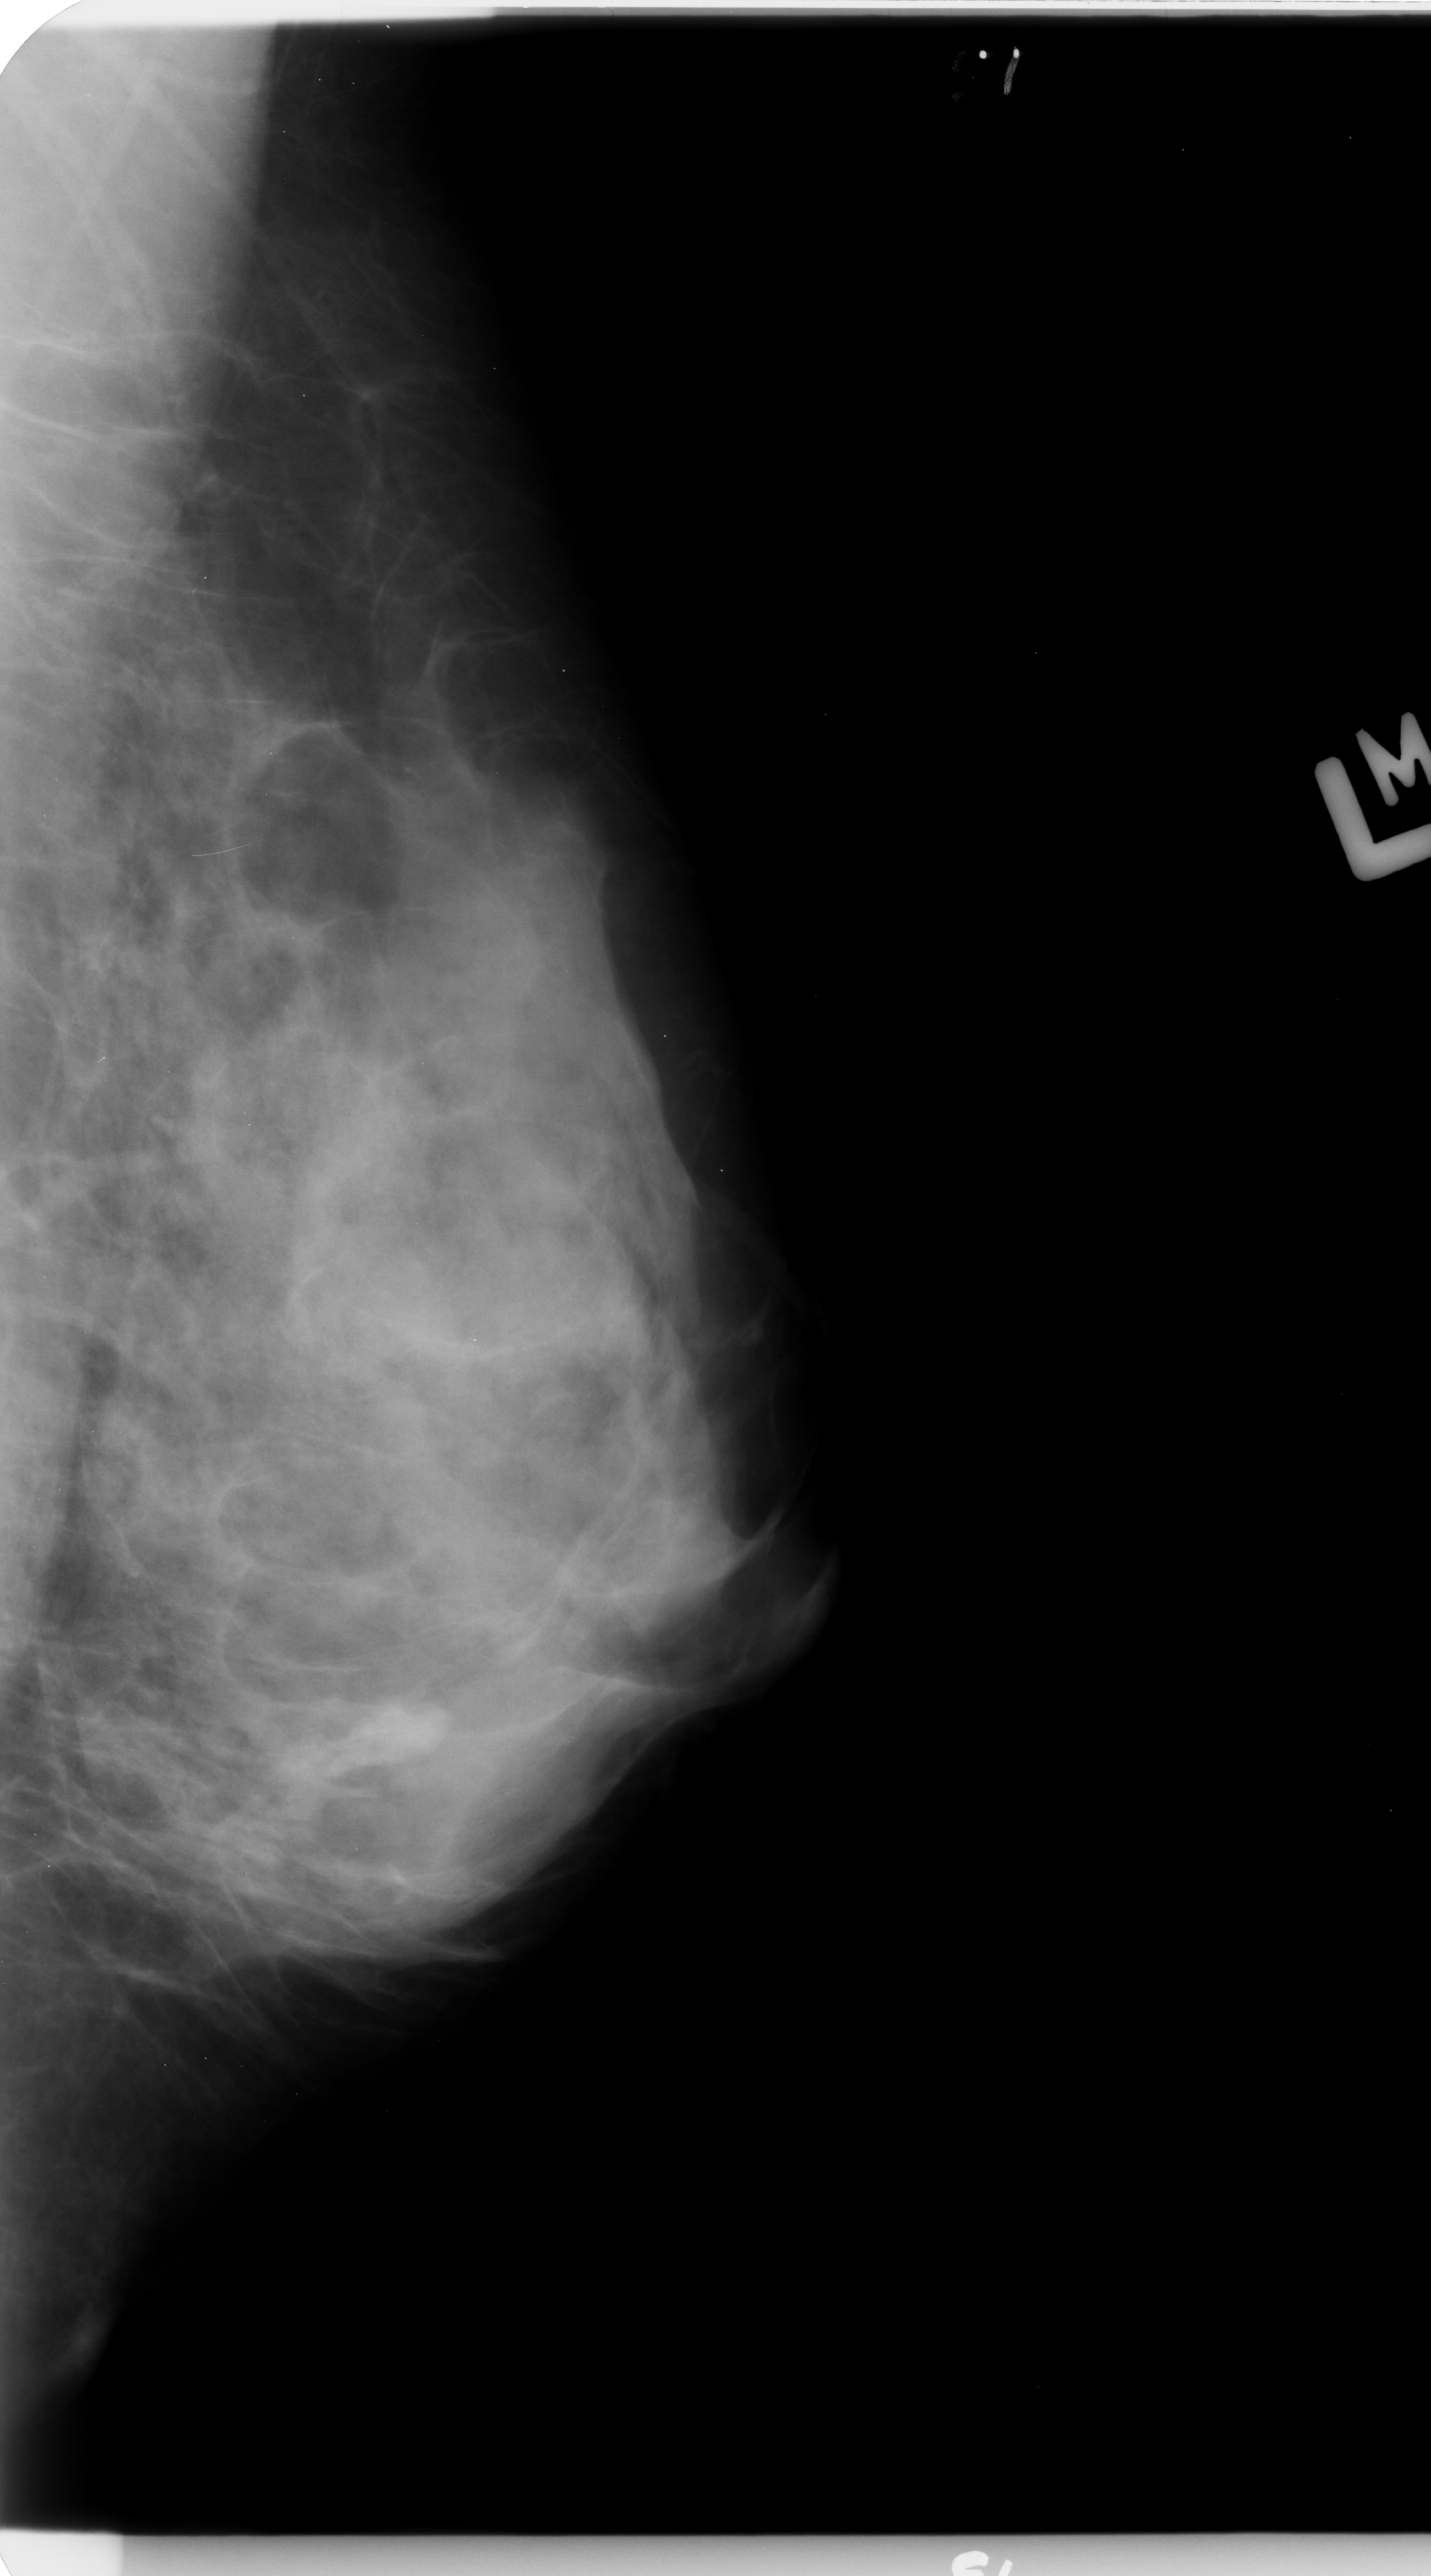
Digitized screen-film mammogram. Left breast. MLO view. Breast composition: extremely dense (BI-RADS density category 4 of 4). 1431 × 2576 image matrix.
Marked abnormalities (boxes around the expert regions of interest):
- mass, shape irregular, margins circumscribed / obscured; BI-RADS assessment category 4; pathology (as recorded): benign: bounding box (x1, y1, x2, y2) in pixels: (298, 1673, 482, 1793)